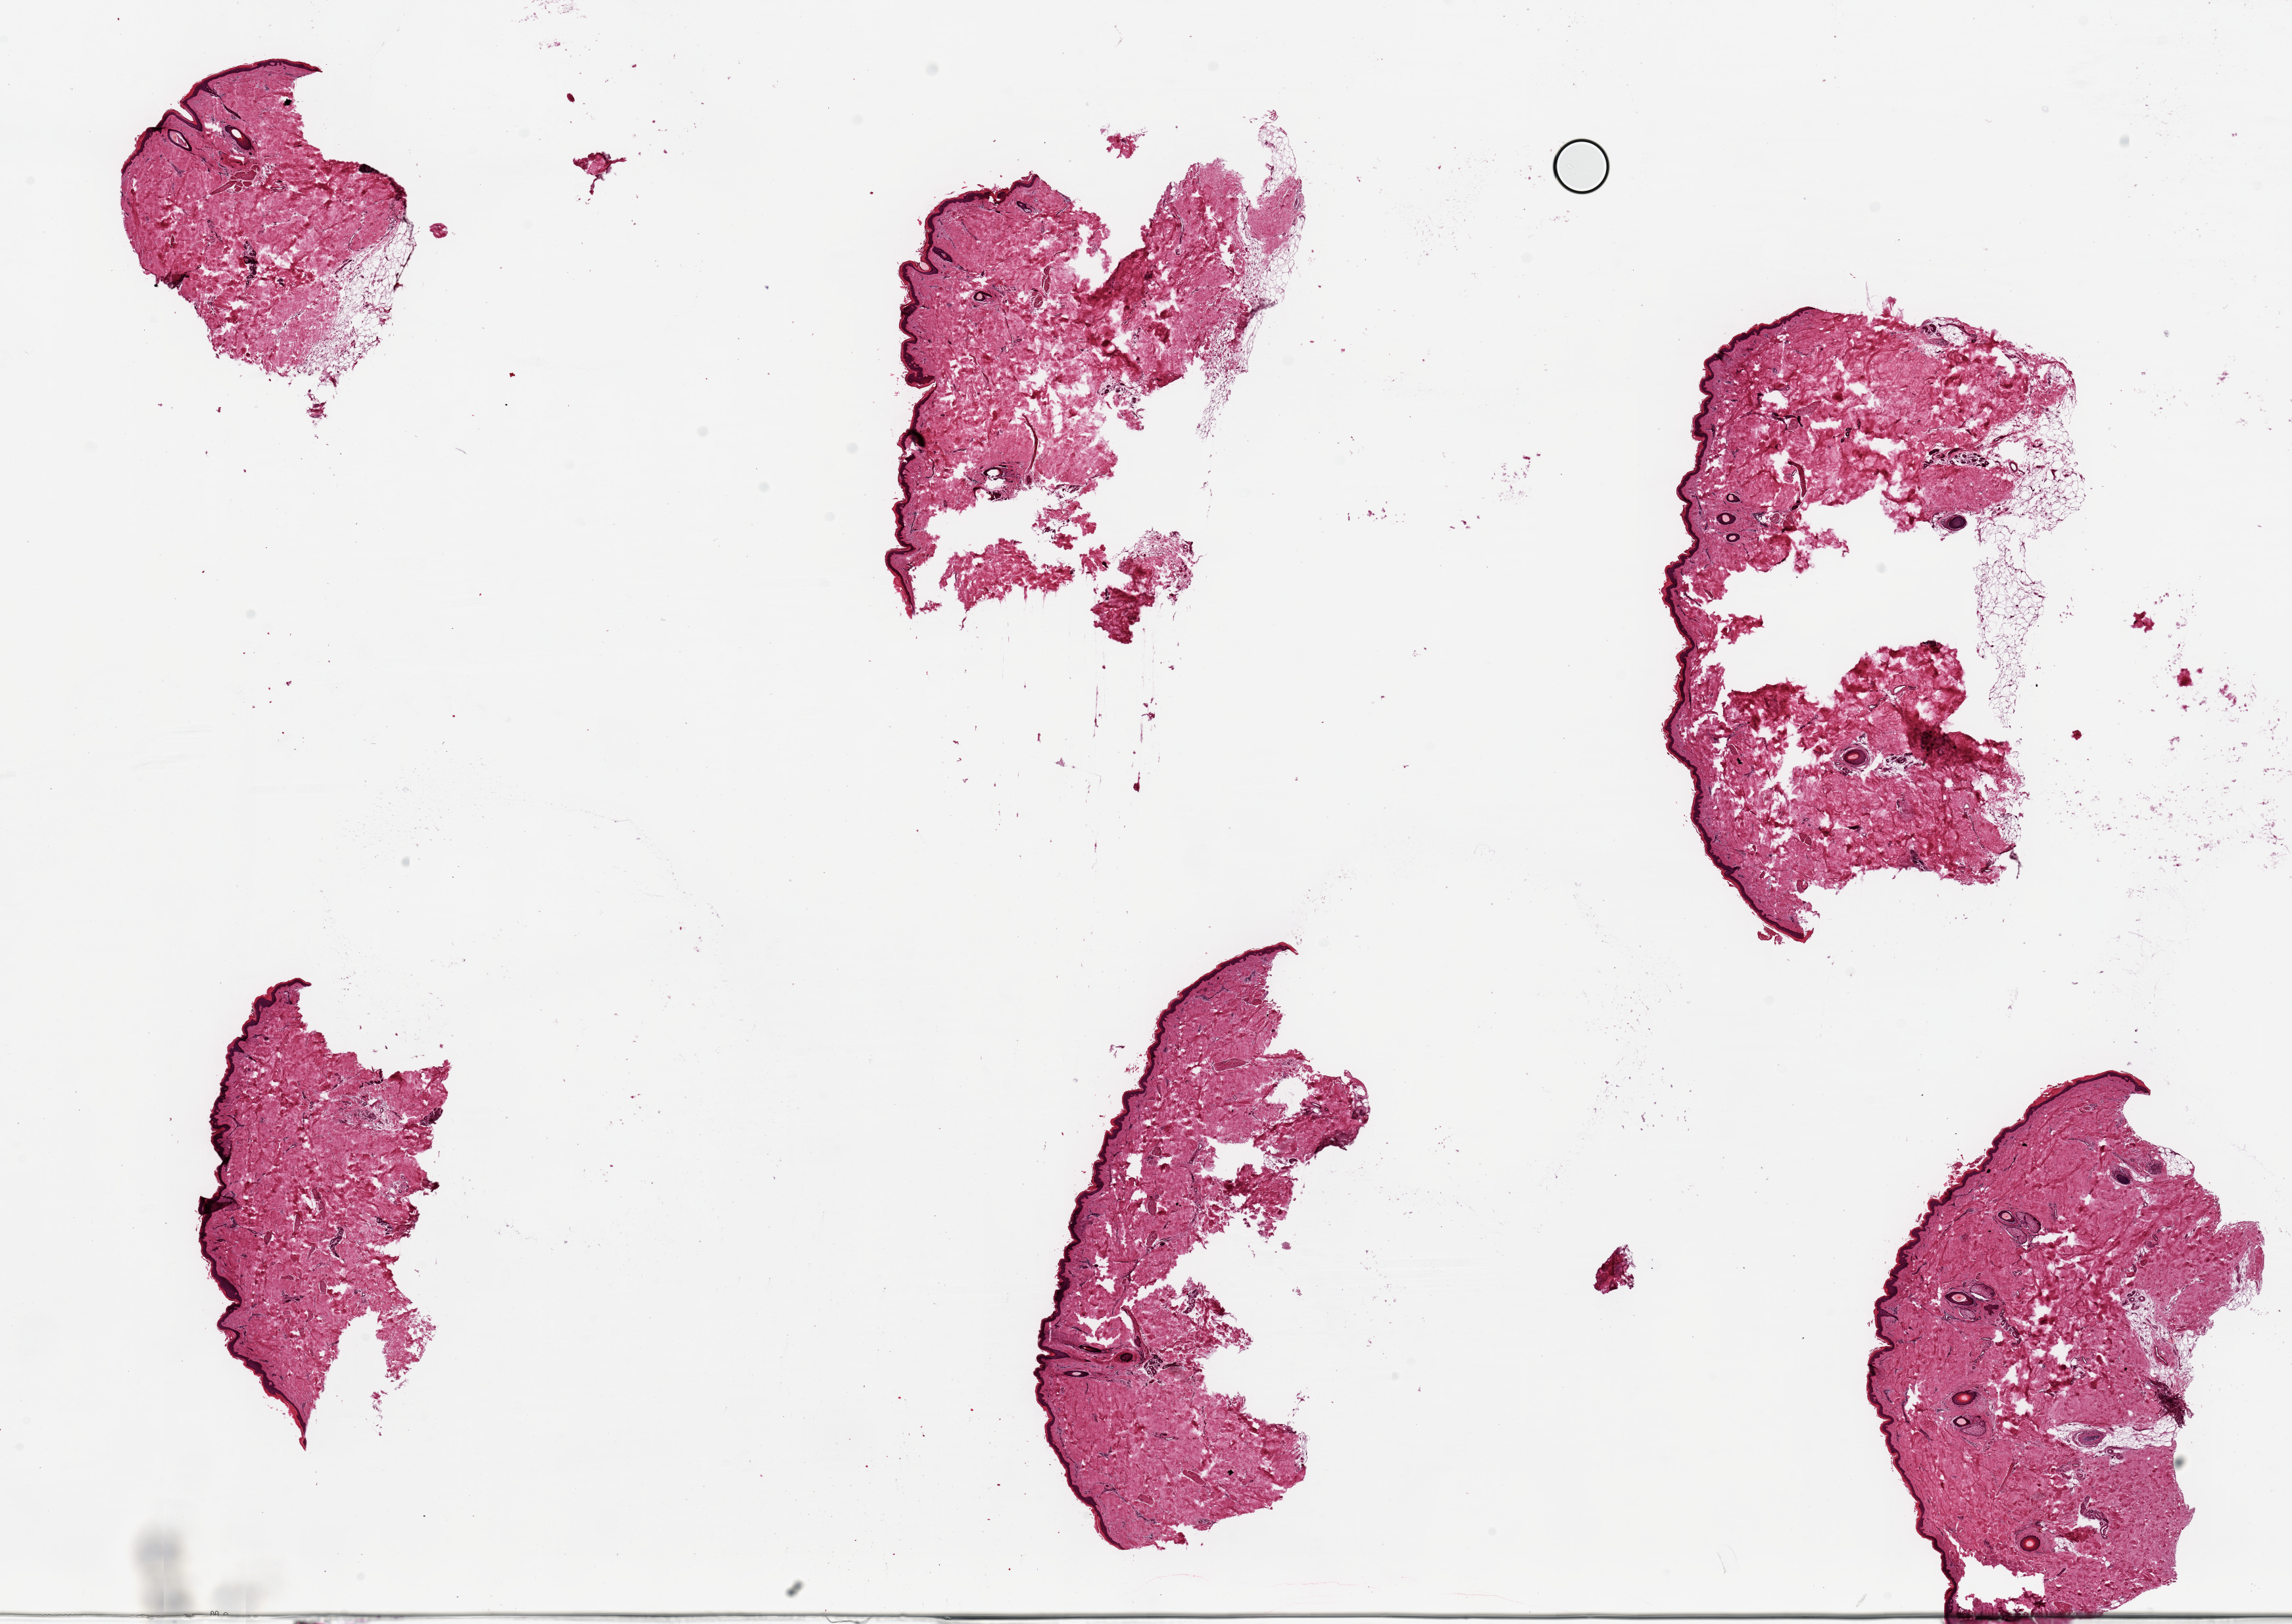
H&E whole-slide image — shown as a low-resolution overview of the whole scanned area (about 27.6 x 19.5 mm, from a 20x scan), PAXgene-fixed, paraffin-embedded tissue, sampled site (target tissue): skin of lower leg, tissue donor sample. Donor: male.
Review note (as recorded): 6 pieces ~8x4mm, squamous epithelium is ~1-2% thickness.